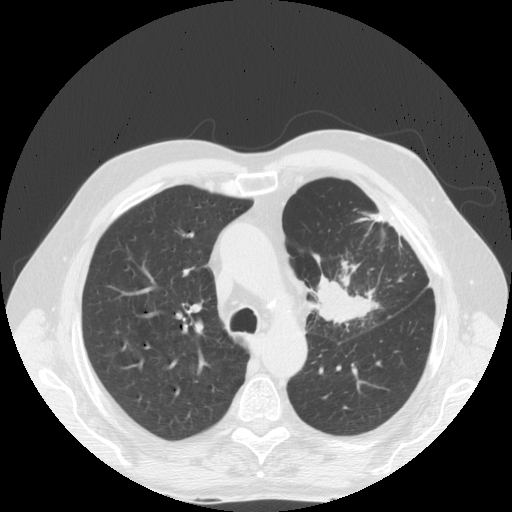
Chest CT (low-dose screening protocol), one axial image. Baseline annual screen. Lung window (W 1500 / L -600 HU). 2.5 mm slice thickness. Standard (soft-tissue) reconstruction kernel (STANDARD). Slice 51 of 171 in the series. 512 × 512 image matrix, field of view 380 × 380 mm. Male, age 70 years at enrolment.
• Expert-annotated lung lesion, box from (x=294, y=255) to (x=391, y=343) px.
• The exam's reader record, not a measurement of the box and not confirmed to be the same lesion: non-calcified nodule or mass ≥4 mm, left upper lobe, 46 × 31 mm, spiculated (stellate) margins, soft tissue attenuation.
• Official screen result: positive, change unspecified: nodule(s) >= 4 mm or enlarging nodule(s), mass(es), or other non-specific abnormalities suspicious for lung cancer.